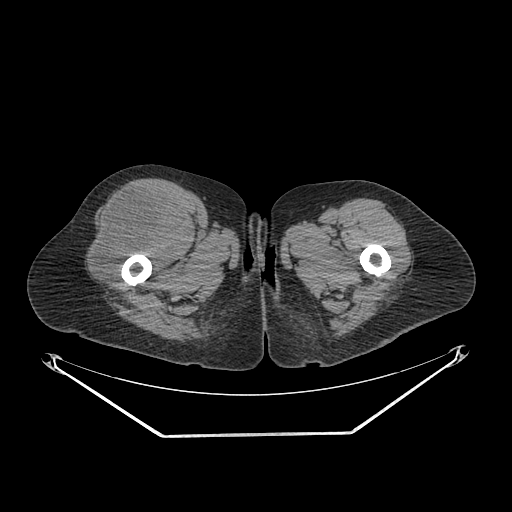
CT of an extremity soft-tissue mass (from a PET/CT study), one axial slice. Slice 267 of 311 in the series (ordered by position). Reconstruction kernel SOFT. Soft-tissue window (W 400 / L 40 HU). 3.75 mm slice thickness. 512 × 512 image matrix, field of view 500 × 500 mm. Female patient. Case-level facts recorded for this patient, not image findings: histological type: pleiomorphic undifferentiated sarcoma; grade: high; site of the primary tumour: right quadricep.
Annotated regions visible in this slice (expert contour drawn on MRI and transferred to this co-registered scan by the dataset authors):
- tumour plus oedema (research contour): bounding box (x1, y1, x2, y2) in pixels: (93, 189, 184, 277)
- tumour (research contour): (93, 189, 184, 277)